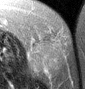
MRI of an extremity soft-tissue mass, one axial slice. Position 14 of 46 along the scan axis. T2-weighted fat-saturated. MR volume resampled by the dataset authors to the PET/CT grid (not the native acquisition matrix). 3.27 mm slice thickness. 85 × 89 image matrix, field of view 83 × 87 mm. Female patient. From the clinical record (not read from this slice): histological type: leiomyosarcoma; grade: intermediate; site of the primary tumour: parascapusular.
Outlined on this slice (expert contour drawn on MRI and transferred to this co-registered scan by the dataset authors):
- gross tumour volume including surrounding oedema: bounding box (x1, y1, x2, y2) in pixels: (29, 30, 65, 77)
- gross tumour volume (mass): (29, 39, 65, 74)